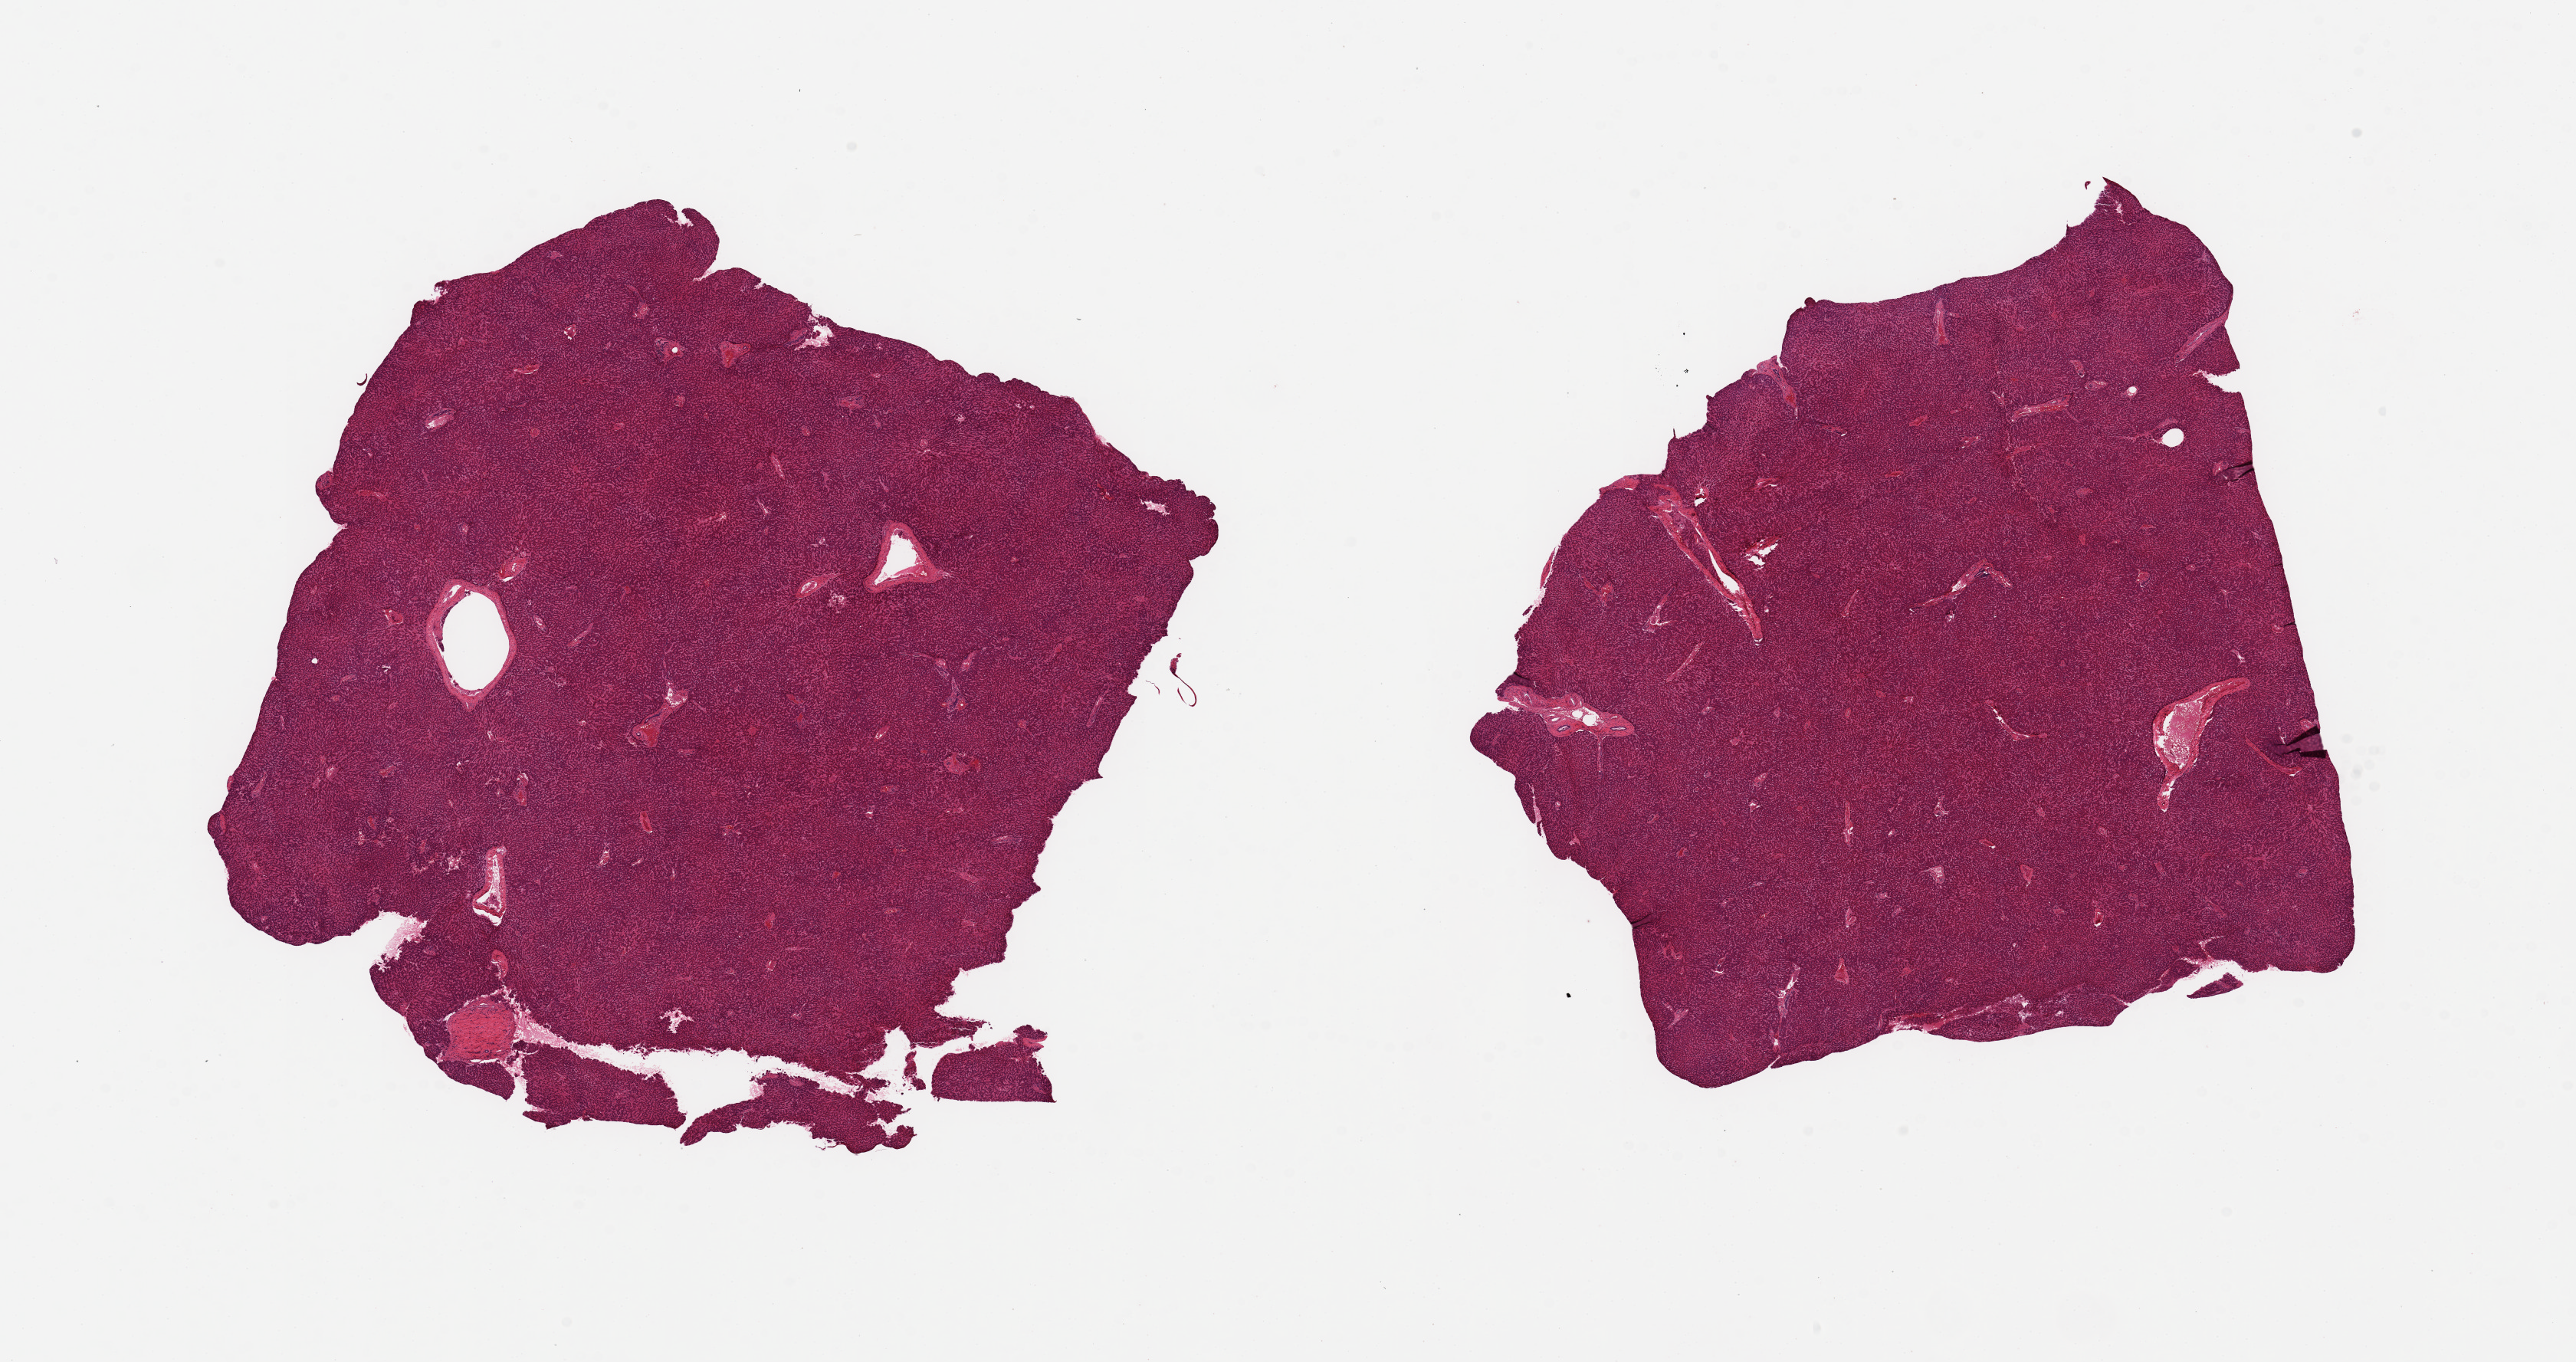
Digitized hematoxylin and eosin (H&E)-stained section, a low-resolution overview of the entire scanned area, about 26.6 x 14.1 mm, PAXgene-fixed paraffin-embedded (PFPE) section, target tissue: liver, donor tissue sample. Donor: female.
Pathologist's review note for this sample: 2 pieces, 8x8 & 8x7mm; no steatosis, no fibrosis.